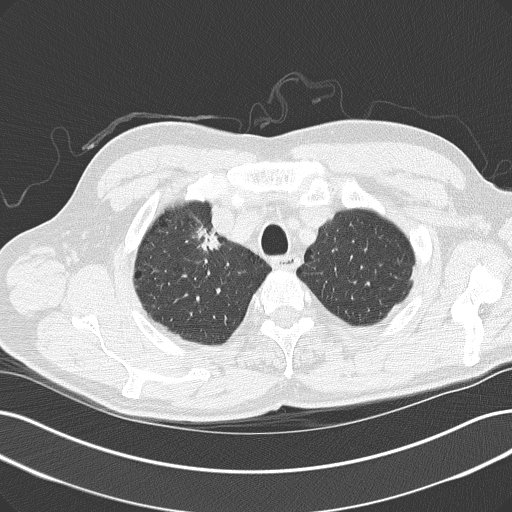
Chest CT (low-dose screening protocol), one axial image. Baseline annual screen. Lung window (W 1500 / L -600 HU). Slice 27 of 152 in the series. Male participant, aged 61 years at enrolment. Current smoker at enrolment.
Lesion marked by an expert reader, bounding box <191,224,246,270> (left, top, right, bottom; pixels). The screening reader recorded 2 non-calcified nodules or masses ≥4 mm on this exam (right upper lobe, right upper lobe); which of them this box marks is not recorded. Official screen result: positive, change unspecified: nodule(s) >= 4 mm or enlarging nodule(s), mass(es), or other non-specific abnormalities suspicious for lung cancer.